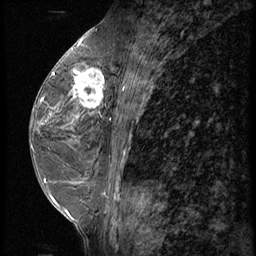
Breast MRI (dynamic contrast-enhanced), one sagittal slice; slice 30 of 62 in the series (ordered by position); 3 images stored at this slice position (order not interpretable as contrast timing); 1.5 T; TE 4.2 ms, TR 9 ms; 2.5 mm slice thickness; 256 × 256 image matrix, field of view 180 × 180 mm. Patient: female, 44 years. Case-level facts recorded for this patient, not image findings: setting: breast cancer imaged before/during neoadjuvant chemotherapy; receptor status: triple-negative.
Structures marked on this image (semi-automatic segmentation, software-assisted and operator-edited):
- analysis volume of interest (the breast-tissue region the enhancement analysis was run in; not a lesion): bounding box <67,64,116,125> (left, top, right, bottom; pixels)
- tumour enhancement mask (voxels above the 140 % enhancement threshold inside the analysis volume of interest): <69,68,105,118>